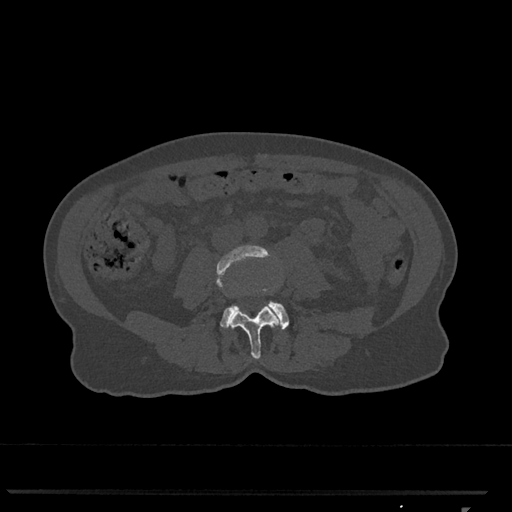
CT including the spine, one axial slice. Slice 245 of 793 in the series (ordered by position). Reconstruction kernel Br40s/3. 120 kVp. Bone window (W 1800 / L 400 HU). 0.5 mm slice thickness. 512 × 512 image matrix, field of view 380 × 380 mm. Patient: female, 62 years. From the clinical record (not read from this slice): primary cancer: renal.
Annotated regions visible in this slice (semi-automatic segmentation, software-assisted and operator-edited):
- L3 vertebra: box from (x=216, y=245) to (x=282, y=359) px
- L4 vertebra: (x=220, y=288)–(x=289, y=330)